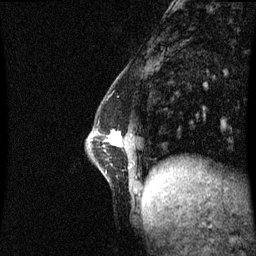
Breast MRI (dynamic contrast-enhanced), one sagittal slice. Position 20 of 60 along the scan axis. Dynamic contrast-enhanced series, image 2 of 3 at this slice position (ordered by acquisition). 1.5 T. TE 4.2 ms, TR 8.9 ms. 2.2 mm slice thickness. 256 × 256 image matrix, field of view 210 × 210 mm. Patient: female, 47 years. From the clinical record (not read from this slice): setting: breast cancer imaged before/during neoadjuvant chemotherapy; receptor status: HR-positive, HER2-negative.
Annotated regions visible in this slice (semi-automatic segmentation, software-assisted and operator-edited):
- analysis volume of interest (the breast-tissue region the enhancement analysis was run in; not a lesion): bounding box [x1, y1, x2, y2] px = [88, 131, 142, 192]
- tumour enhancement mask (voxels above the 70 % enhancement threshold inside the analysis volume of interest): [110, 132, 122, 145]